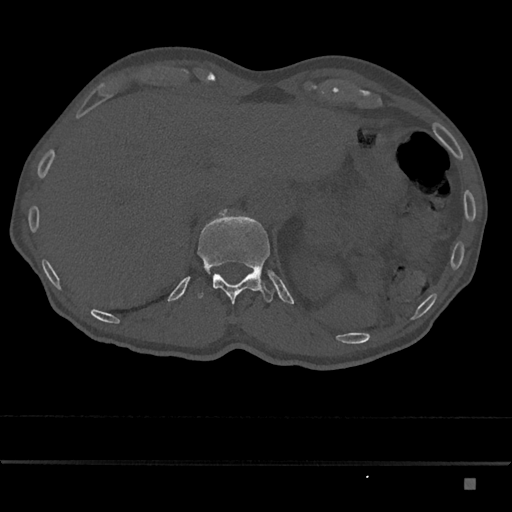
CT including the spine, one axial slice; position 611 of 797 along the scan axis; 120 kVp; bone window (W 1800 / L 400 HU); 0.5 mm slice thickness; 512 × 512 image matrix, field of view 390 × 390 mm. Male patient, age 72 years. From the clinical record (not read from this slice): primary cancer: prostate.
Structures marked on this image (semi-automatically segmented with operator editing):
- T12 vertebra: bounding box (x1, y1, x2, y2) in pixels: (197, 213, 274, 305)